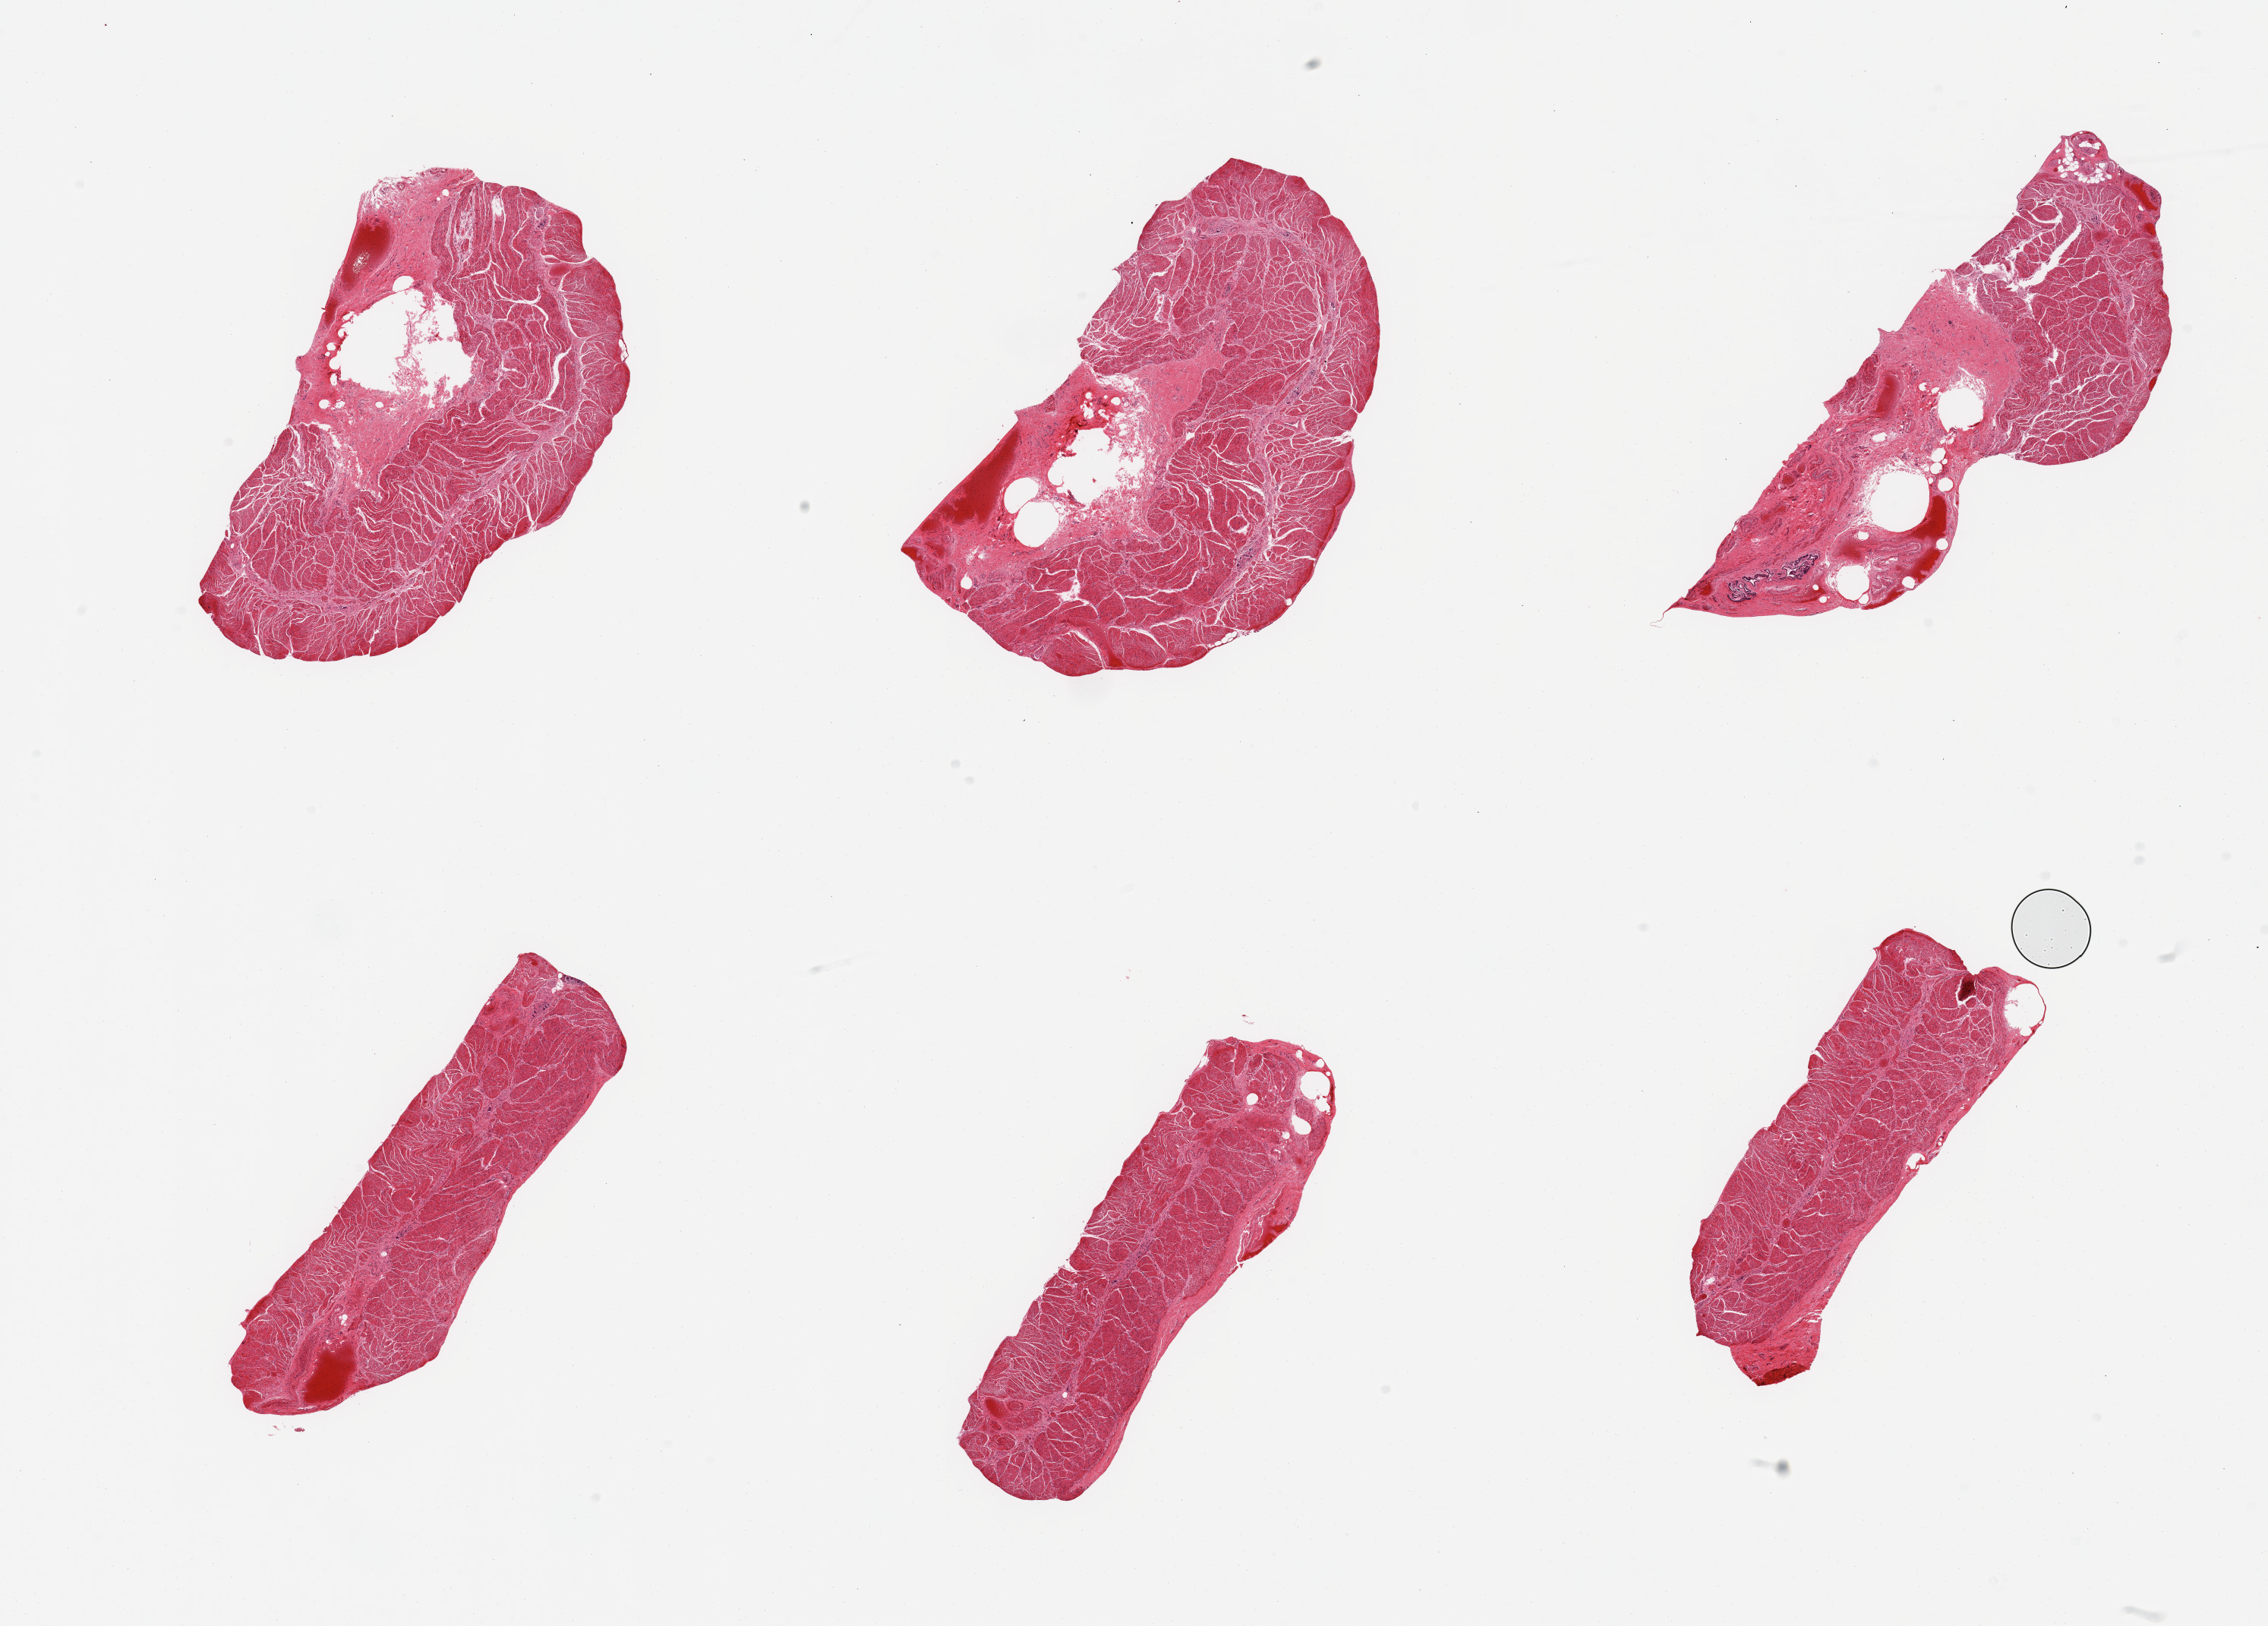
Whole-slide image, H&E stain, brightfield — whole scanned area (about 23.6 x 16.9 mm) shown as a low-resolution overview, PAXgene-fixed paraffin-embedded (PFPE) section, section of esophageal muscle (target tissue), donor tissue sample. Donor: male.
• pathologist's review note for this sample: 6 pieces; target muscularis; congested submucosa on 3 of 6